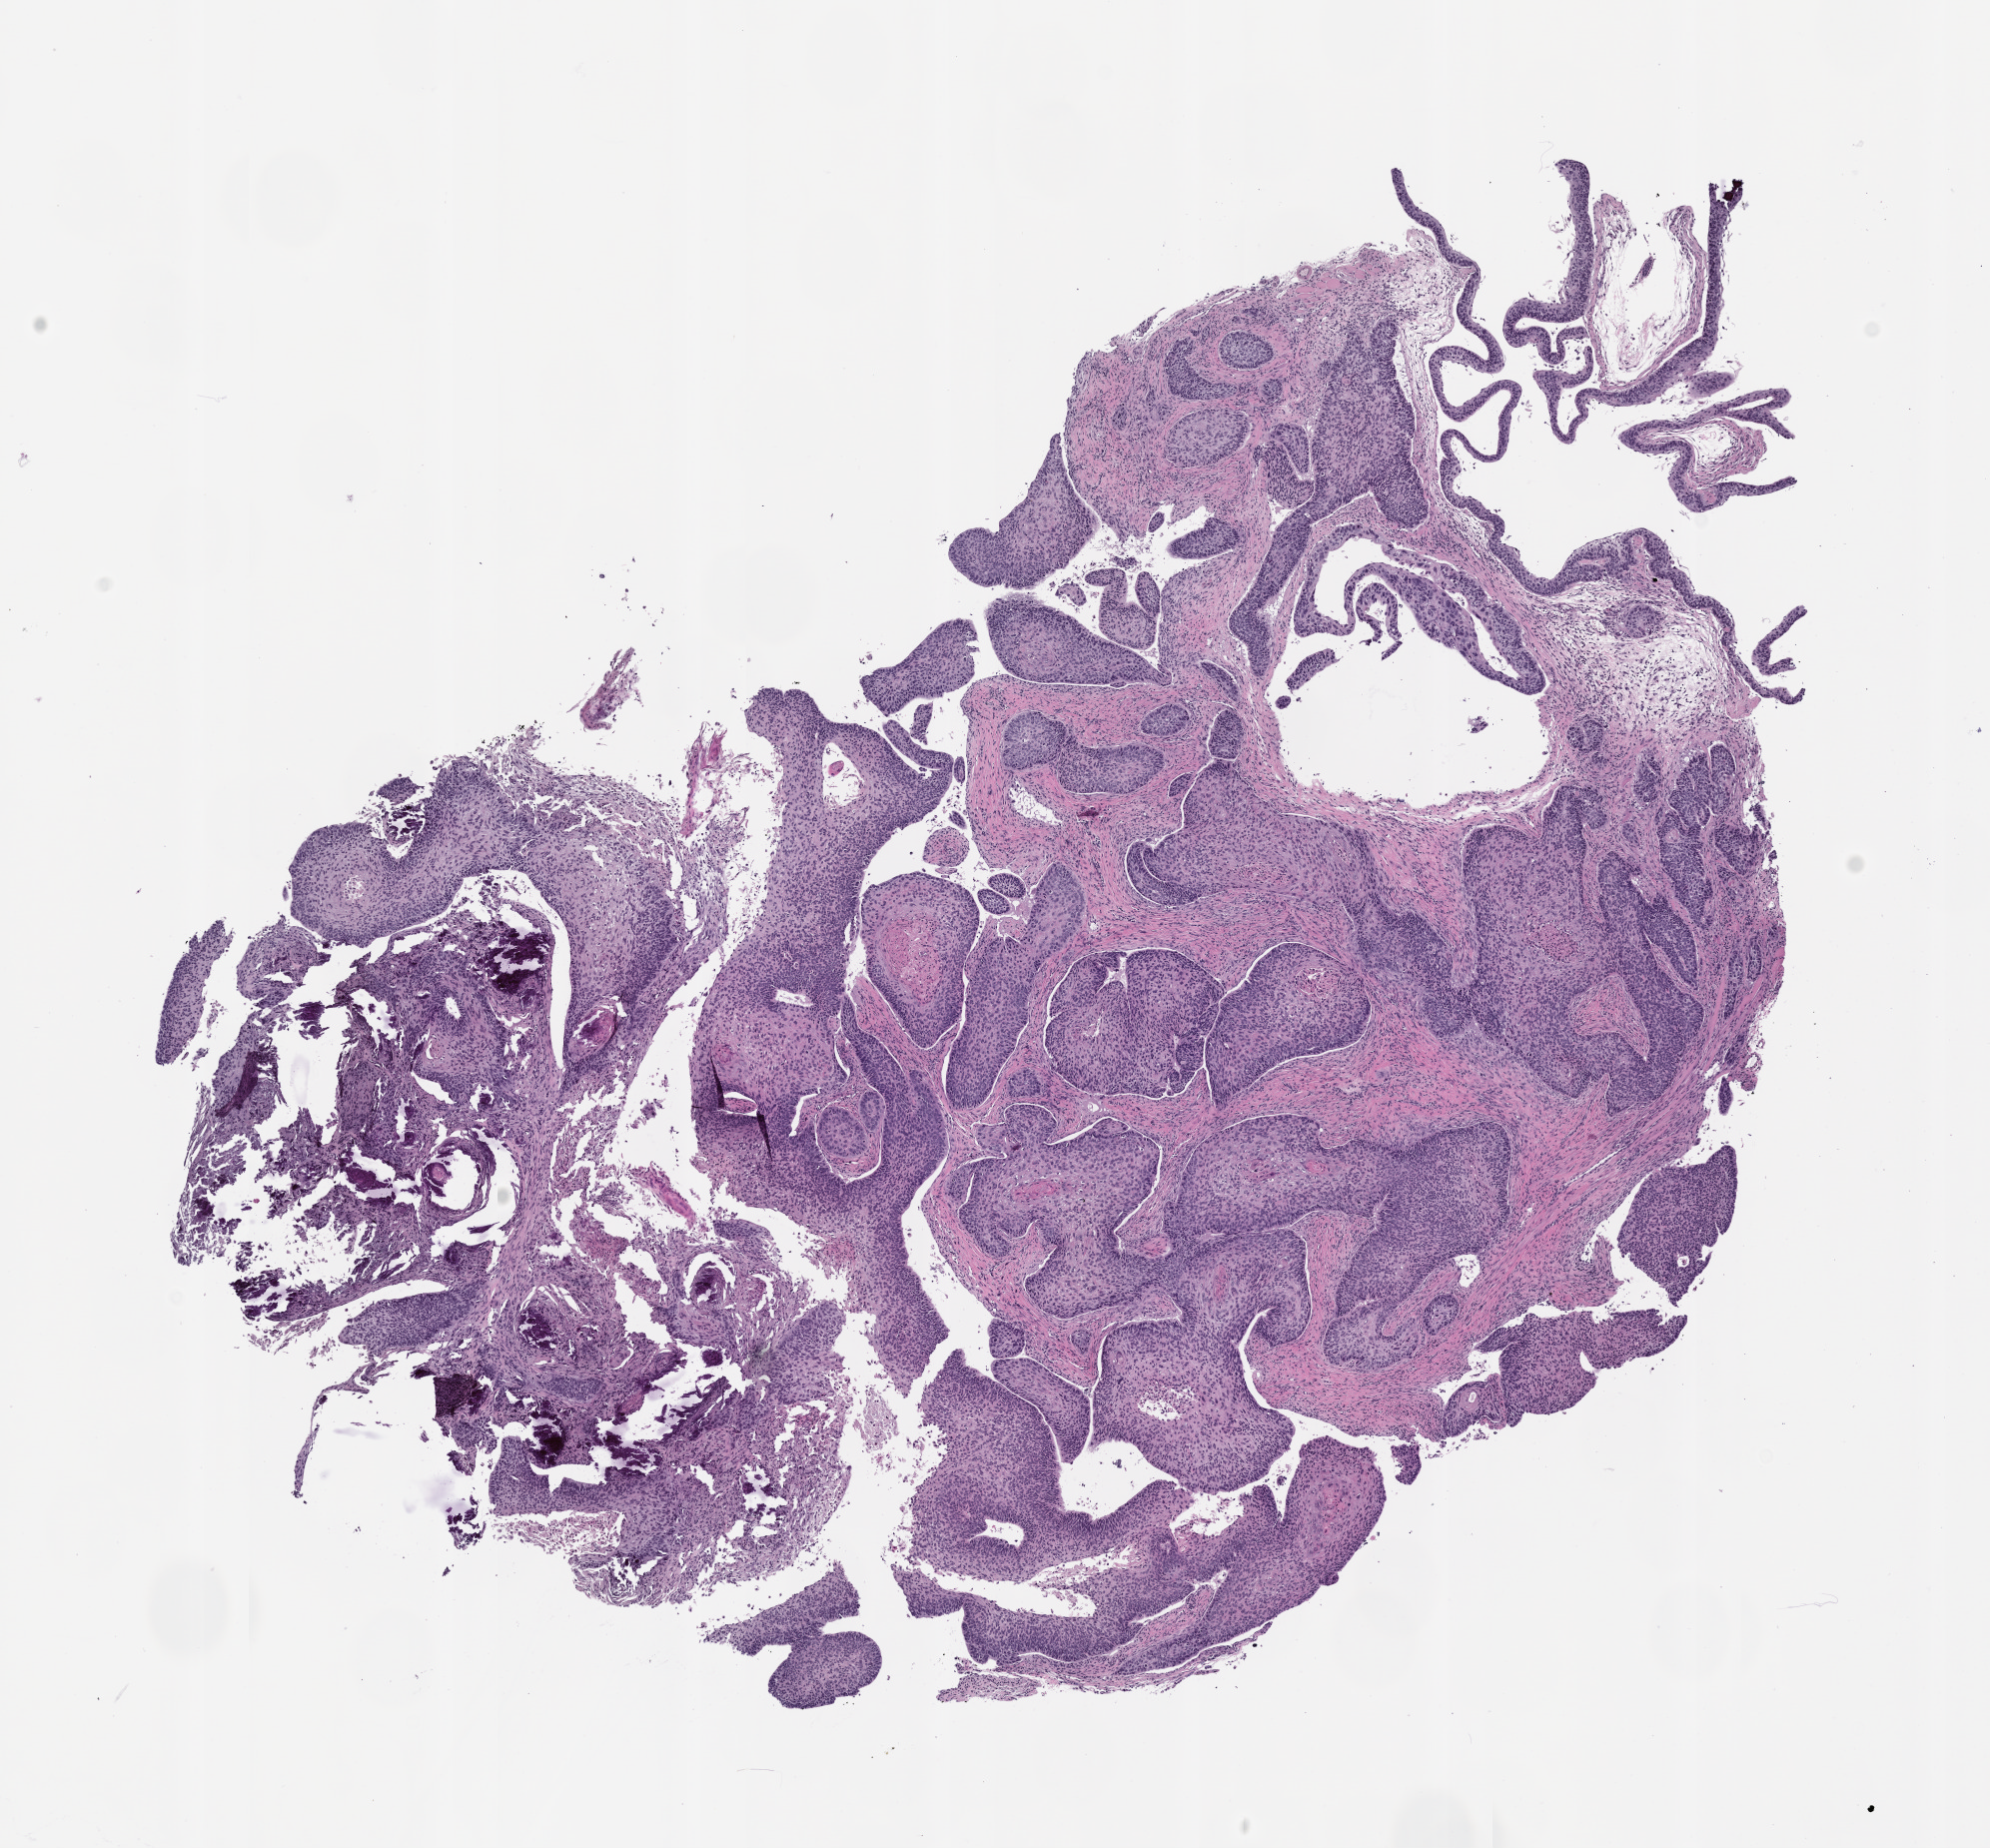
Whole-slide image, hematoxylin and eosin (H&E): patient-derived xenograft (human tumor grown in a mouse), passage 1 — whole scanned area (about 8.0 x 7.4 mm) shown as a low-resolution overview. Formalin-fixed paraffin-embedded section. Originating tumor site category: head and neck.
Originating patient diagnosis: Head and Neck Squamous Cell Carcinoma.